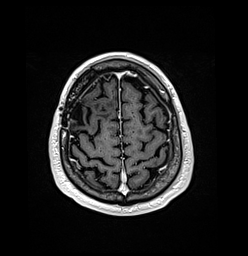
Brain MRI from a brain-tumour surgery series, one axial slice. Slice 32 of 176 in the series (ordered by position). T1-weighted post-contrast. 1 mm slice thickness. 248 × 256 image matrix. Case-level facts recorded for this patient, not image findings: histopathology: Oligodendroglioma; WHO grade: 3; IDH mutation: yes; tumour location: Right Frontal.
Annotated regions visible in this slice (manually delineated by an expert):
- previous resection cavity: bounding box [x1, y1, x2, y2] px = [71, 101, 84, 125]